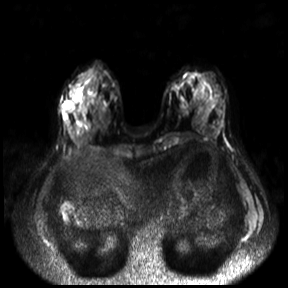
Breast MRI, one axial slice; position 10 of 30 along the scan axis; diffusion-weighted series; image 2 of 4 stored at this slice position (different b-values; order by instance number); 3 T; 4 mm slice thickness; 288 × 288 image matrix, field of view 360 × 360 mm. Female patient.
Outlined on this slice (expert manual segmentation):
- tumour on diffusion-weighted imaging: box from (x=63, y=101) to (x=75, y=111) px